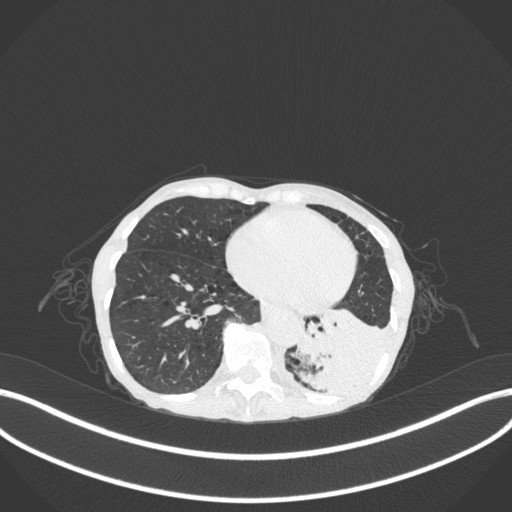
Chest CT, one axial slice. Position 78 of 347 along the scan axis. Reconstruction kernel B31f. Lung window (W 1500 / L -600 HU). 512 × 512 image matrix, field of view 400 × 400 mm. Patient: female, 70 years. From the clinical record (not read from this slice): clinical TNM (as recorded): T3 N0 M0; histopathological grade: G3.
Structures marked on this image (rectangle marked by the reading radiologist):
- lung tumour (recorded histology: small cell carcinoma): box from (x=298, y=300) to (x=399, y=404) px